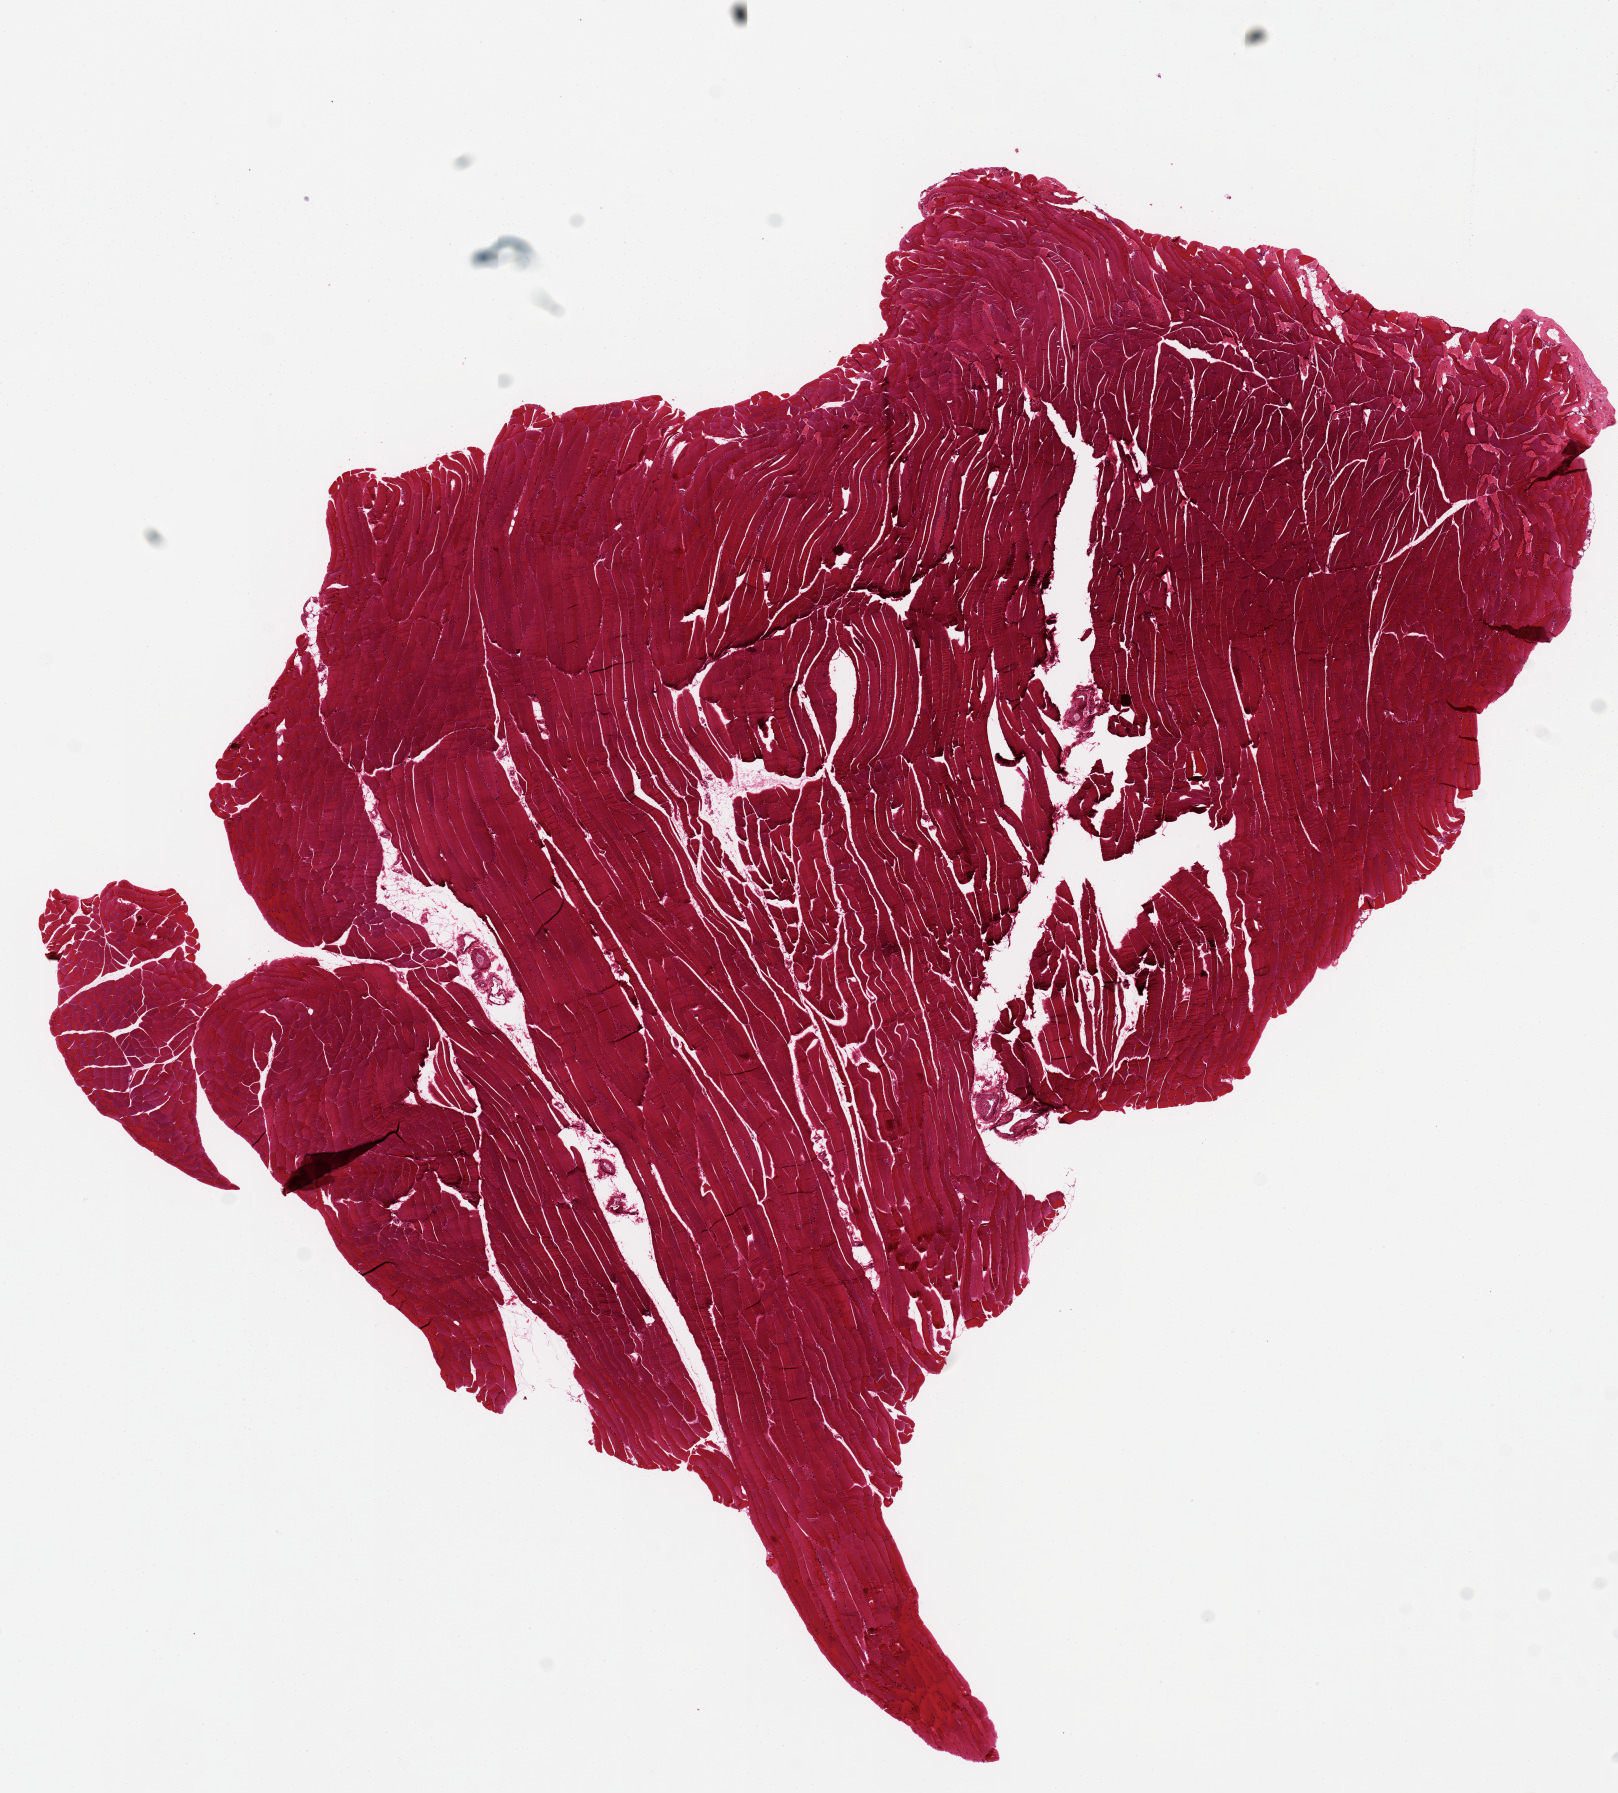
Digitized hematoxylin and eosin (H&E)-stained section, brightfield — shown as a low-resolution overview of the whole scanned area (about 12.8 x 14.2 mm, acquisition: 20x scan); PAXgene-fixed paraffin-embedded (PFPE) section; sampled site (target tissue): skeletal muscle; donor tissue sample. Male donor.
Review note (as recorded): 12x9 mm.